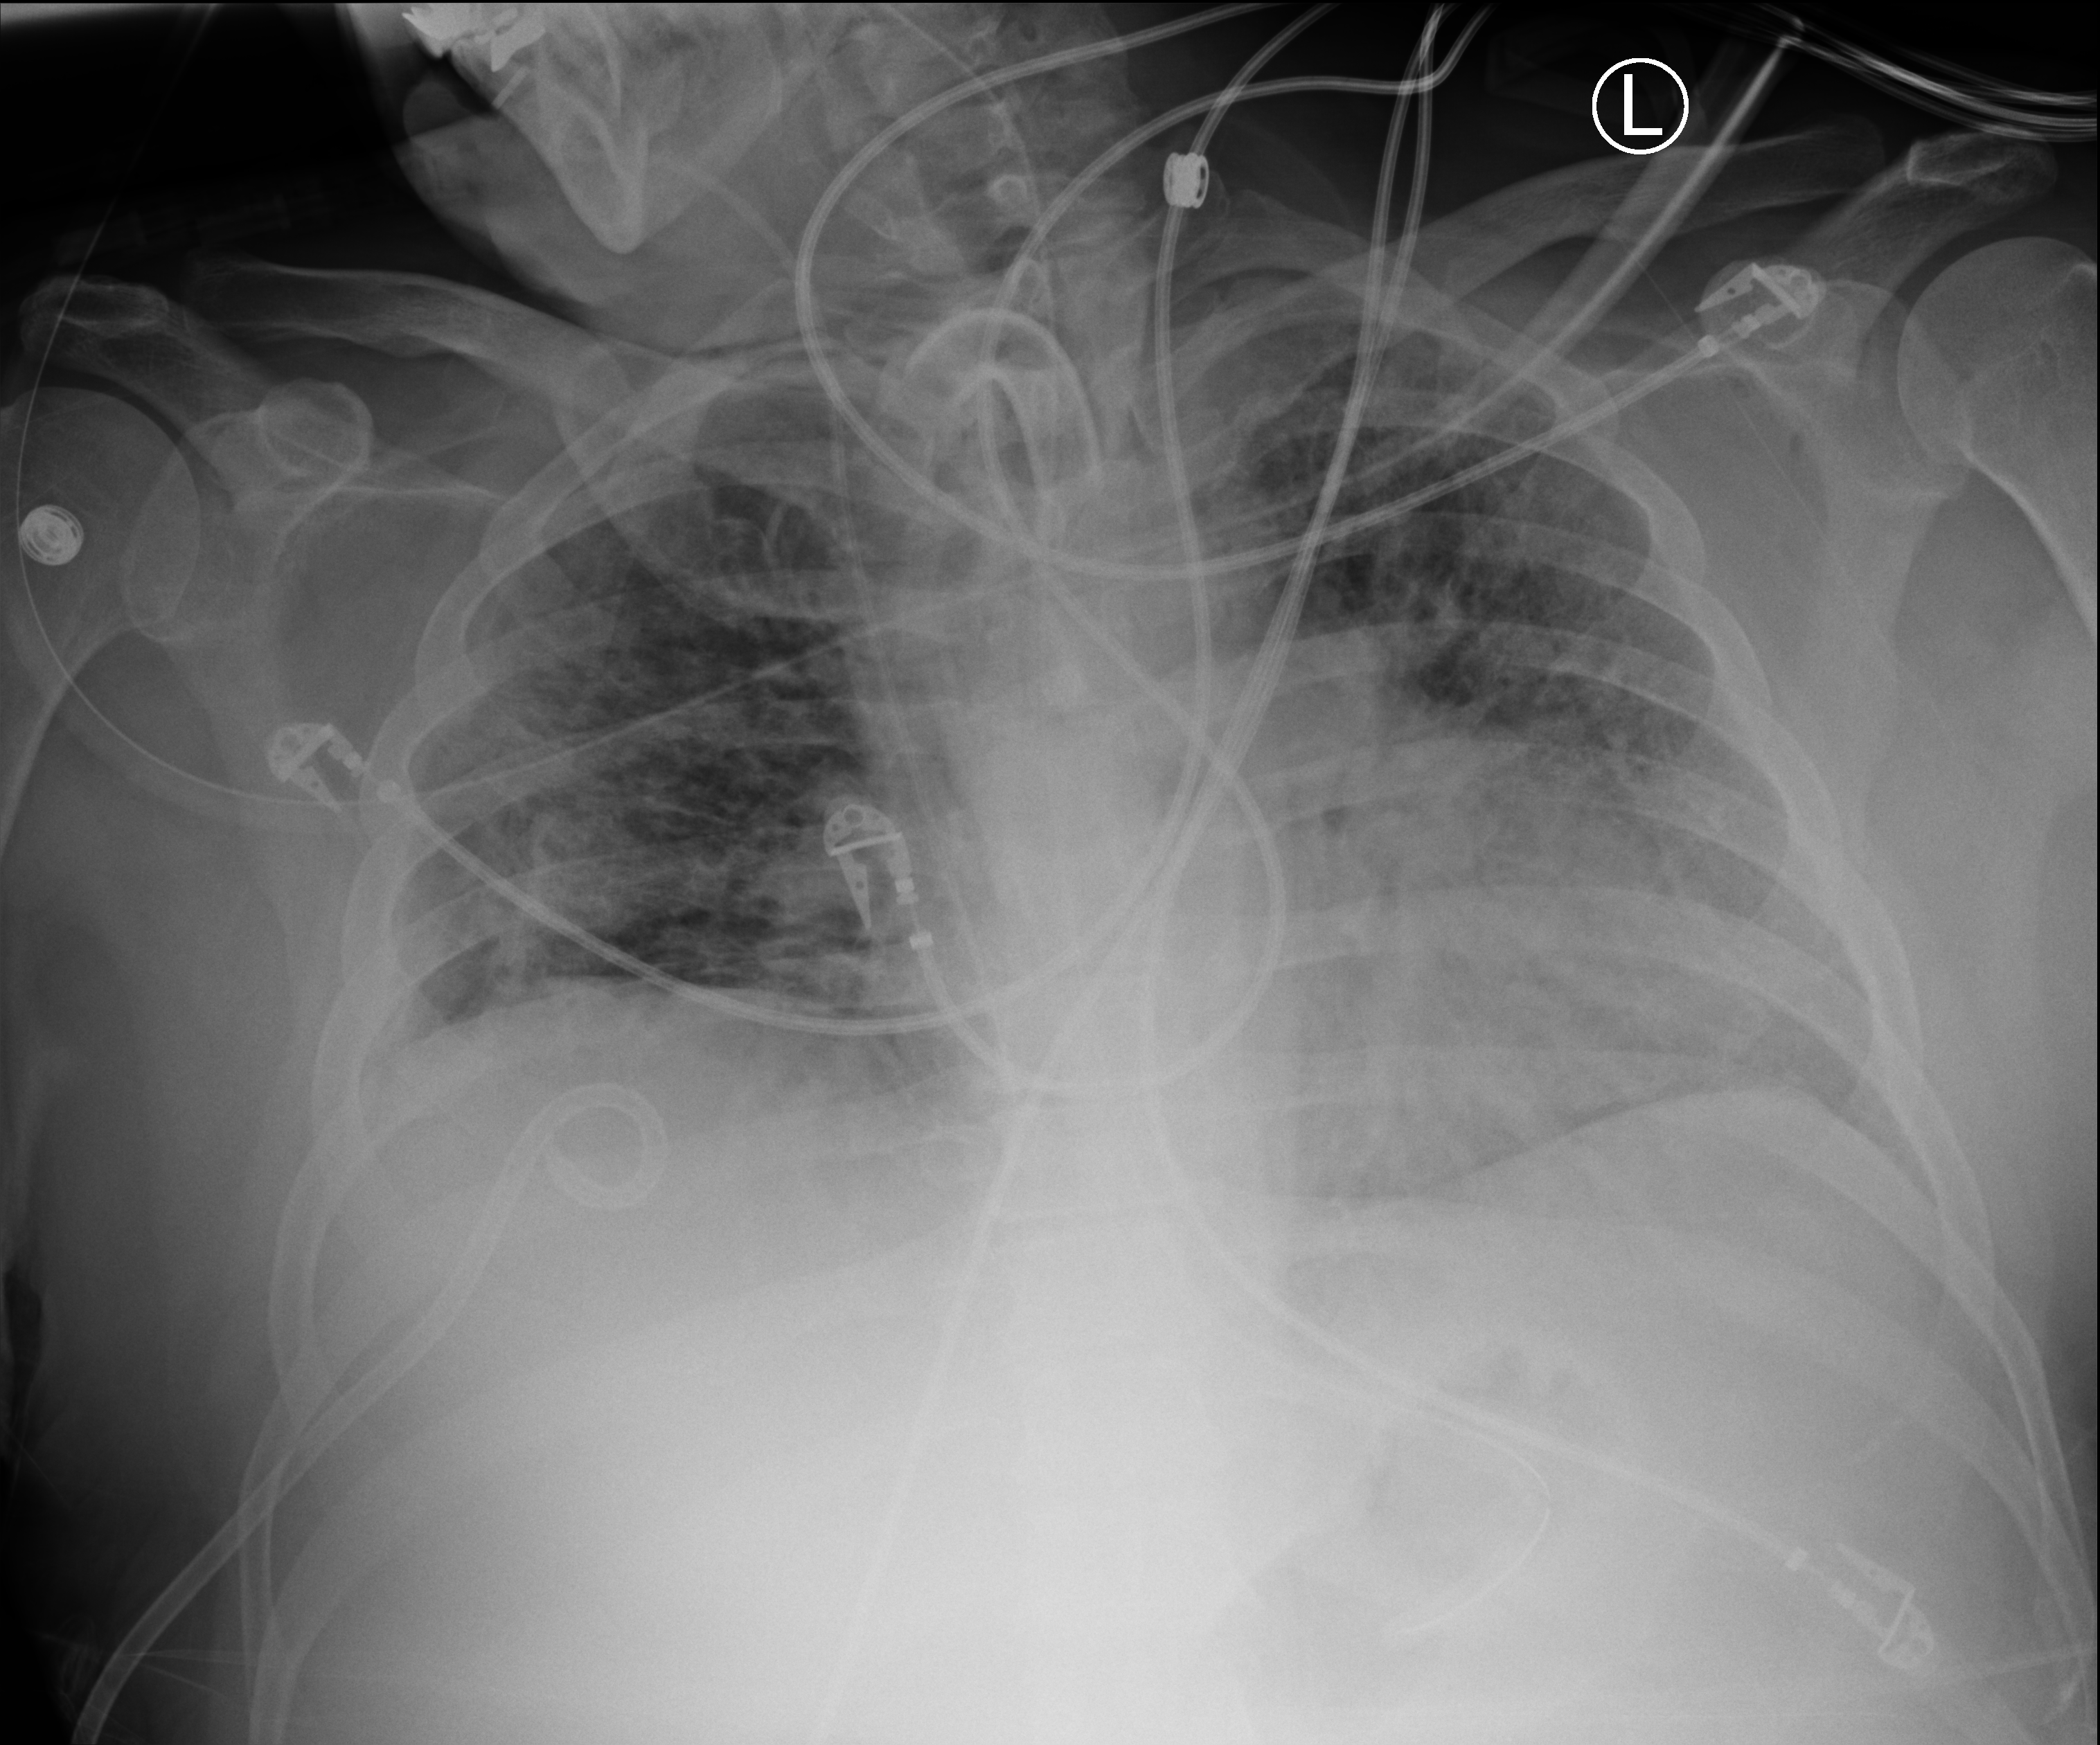
Portable chest radiograph. Male patient hospitalised with COVID-19, age 18–59 years.
From the hospital-stay record, not from the radiograph (when in the stay this image was taken is not recorded): hypertension (admission record): yes.